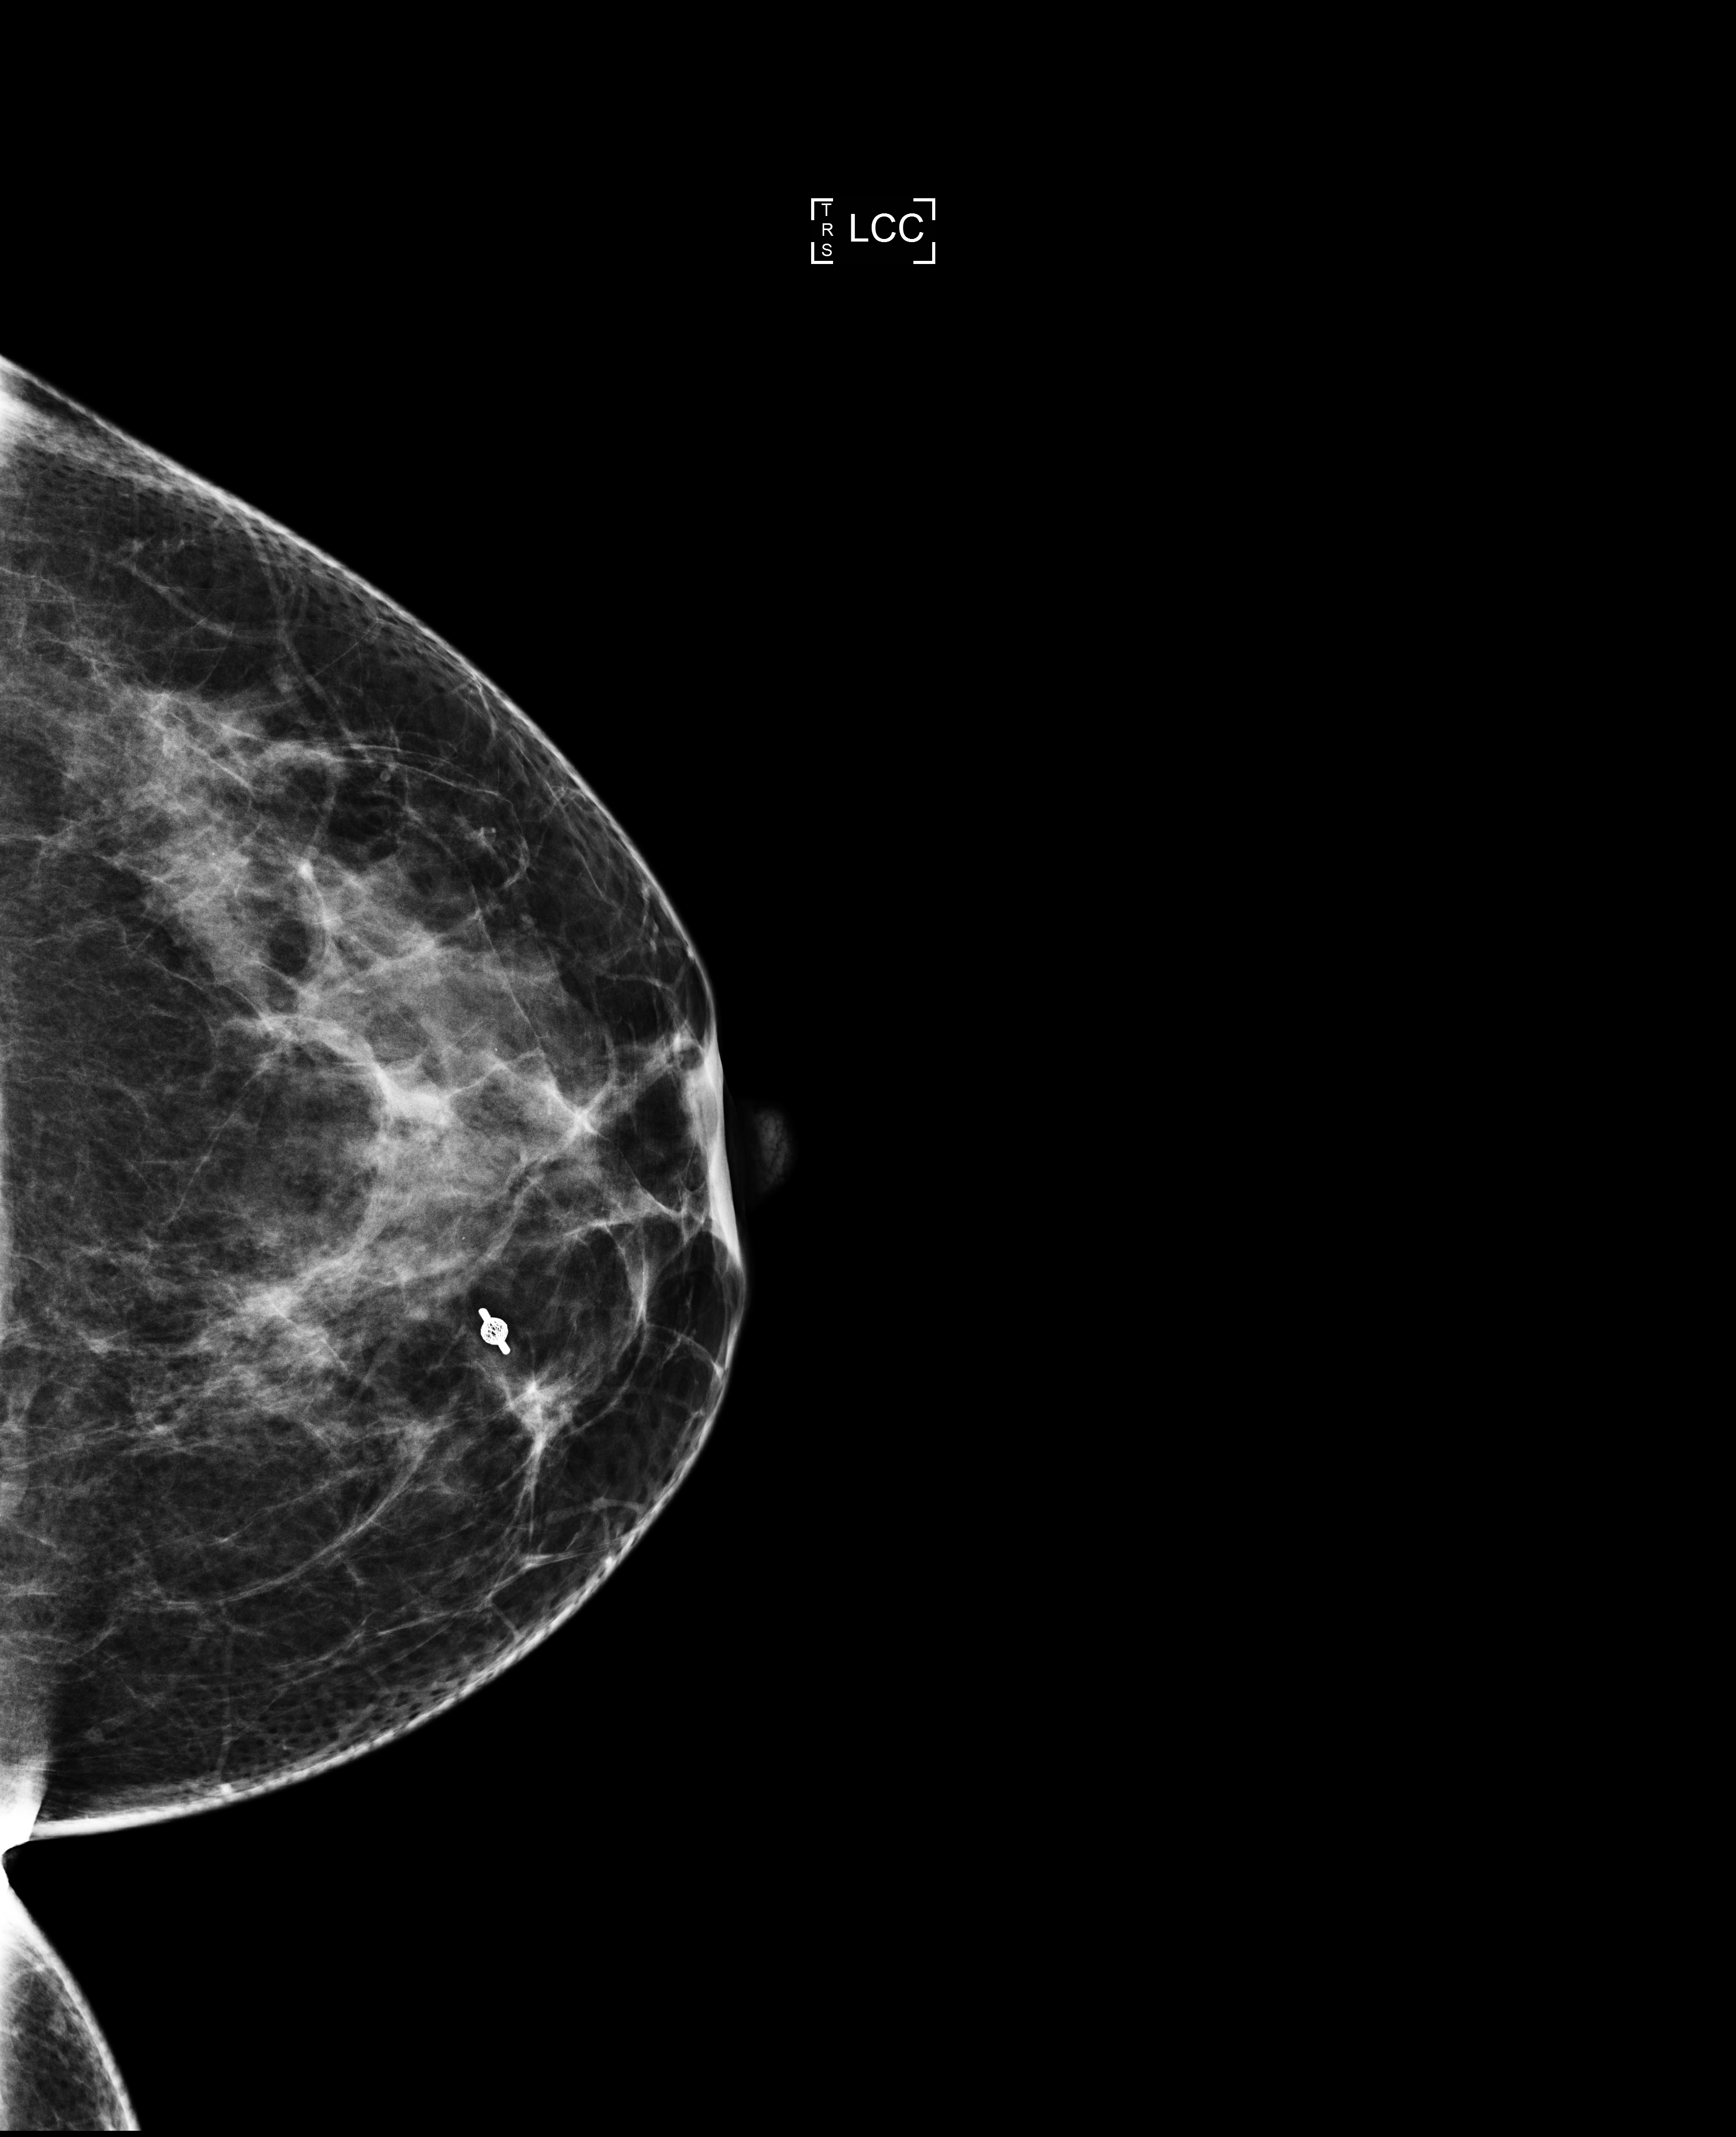
Screening examination, compressed breast thickness 63 mm. Female patient, age 42 years.
Image type: full-field digital mammogram. Breast: left. Projection: cranio-caudal projection.